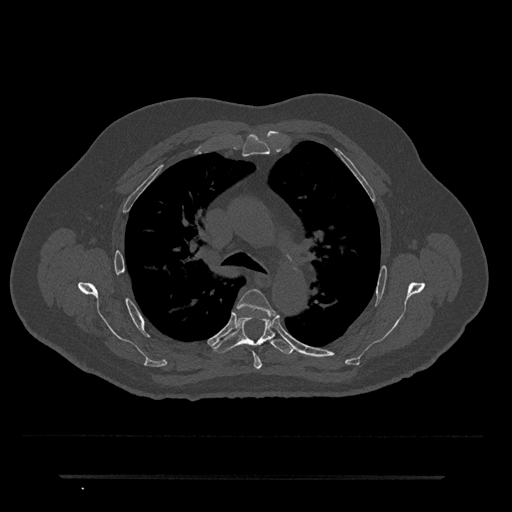
CT including the spine, one axial slice. Slice 501 of 797 in the series (ordered by position). Bone window (W 1800 / L 400 HU). 0.5 mm slice thickness. 512 × 512 image matrix. Patient: male, 69 years. From the clinical record (not read from this slice): primary cancer: prostate.
Outlined on this slice (semi-automatically segmented with operator editing):
- T4 vertebra: box from (x=237, y=289) to (x=277, y=369) px
- T5 vertebra: (x=212, y=316)–(x=296, y=354)